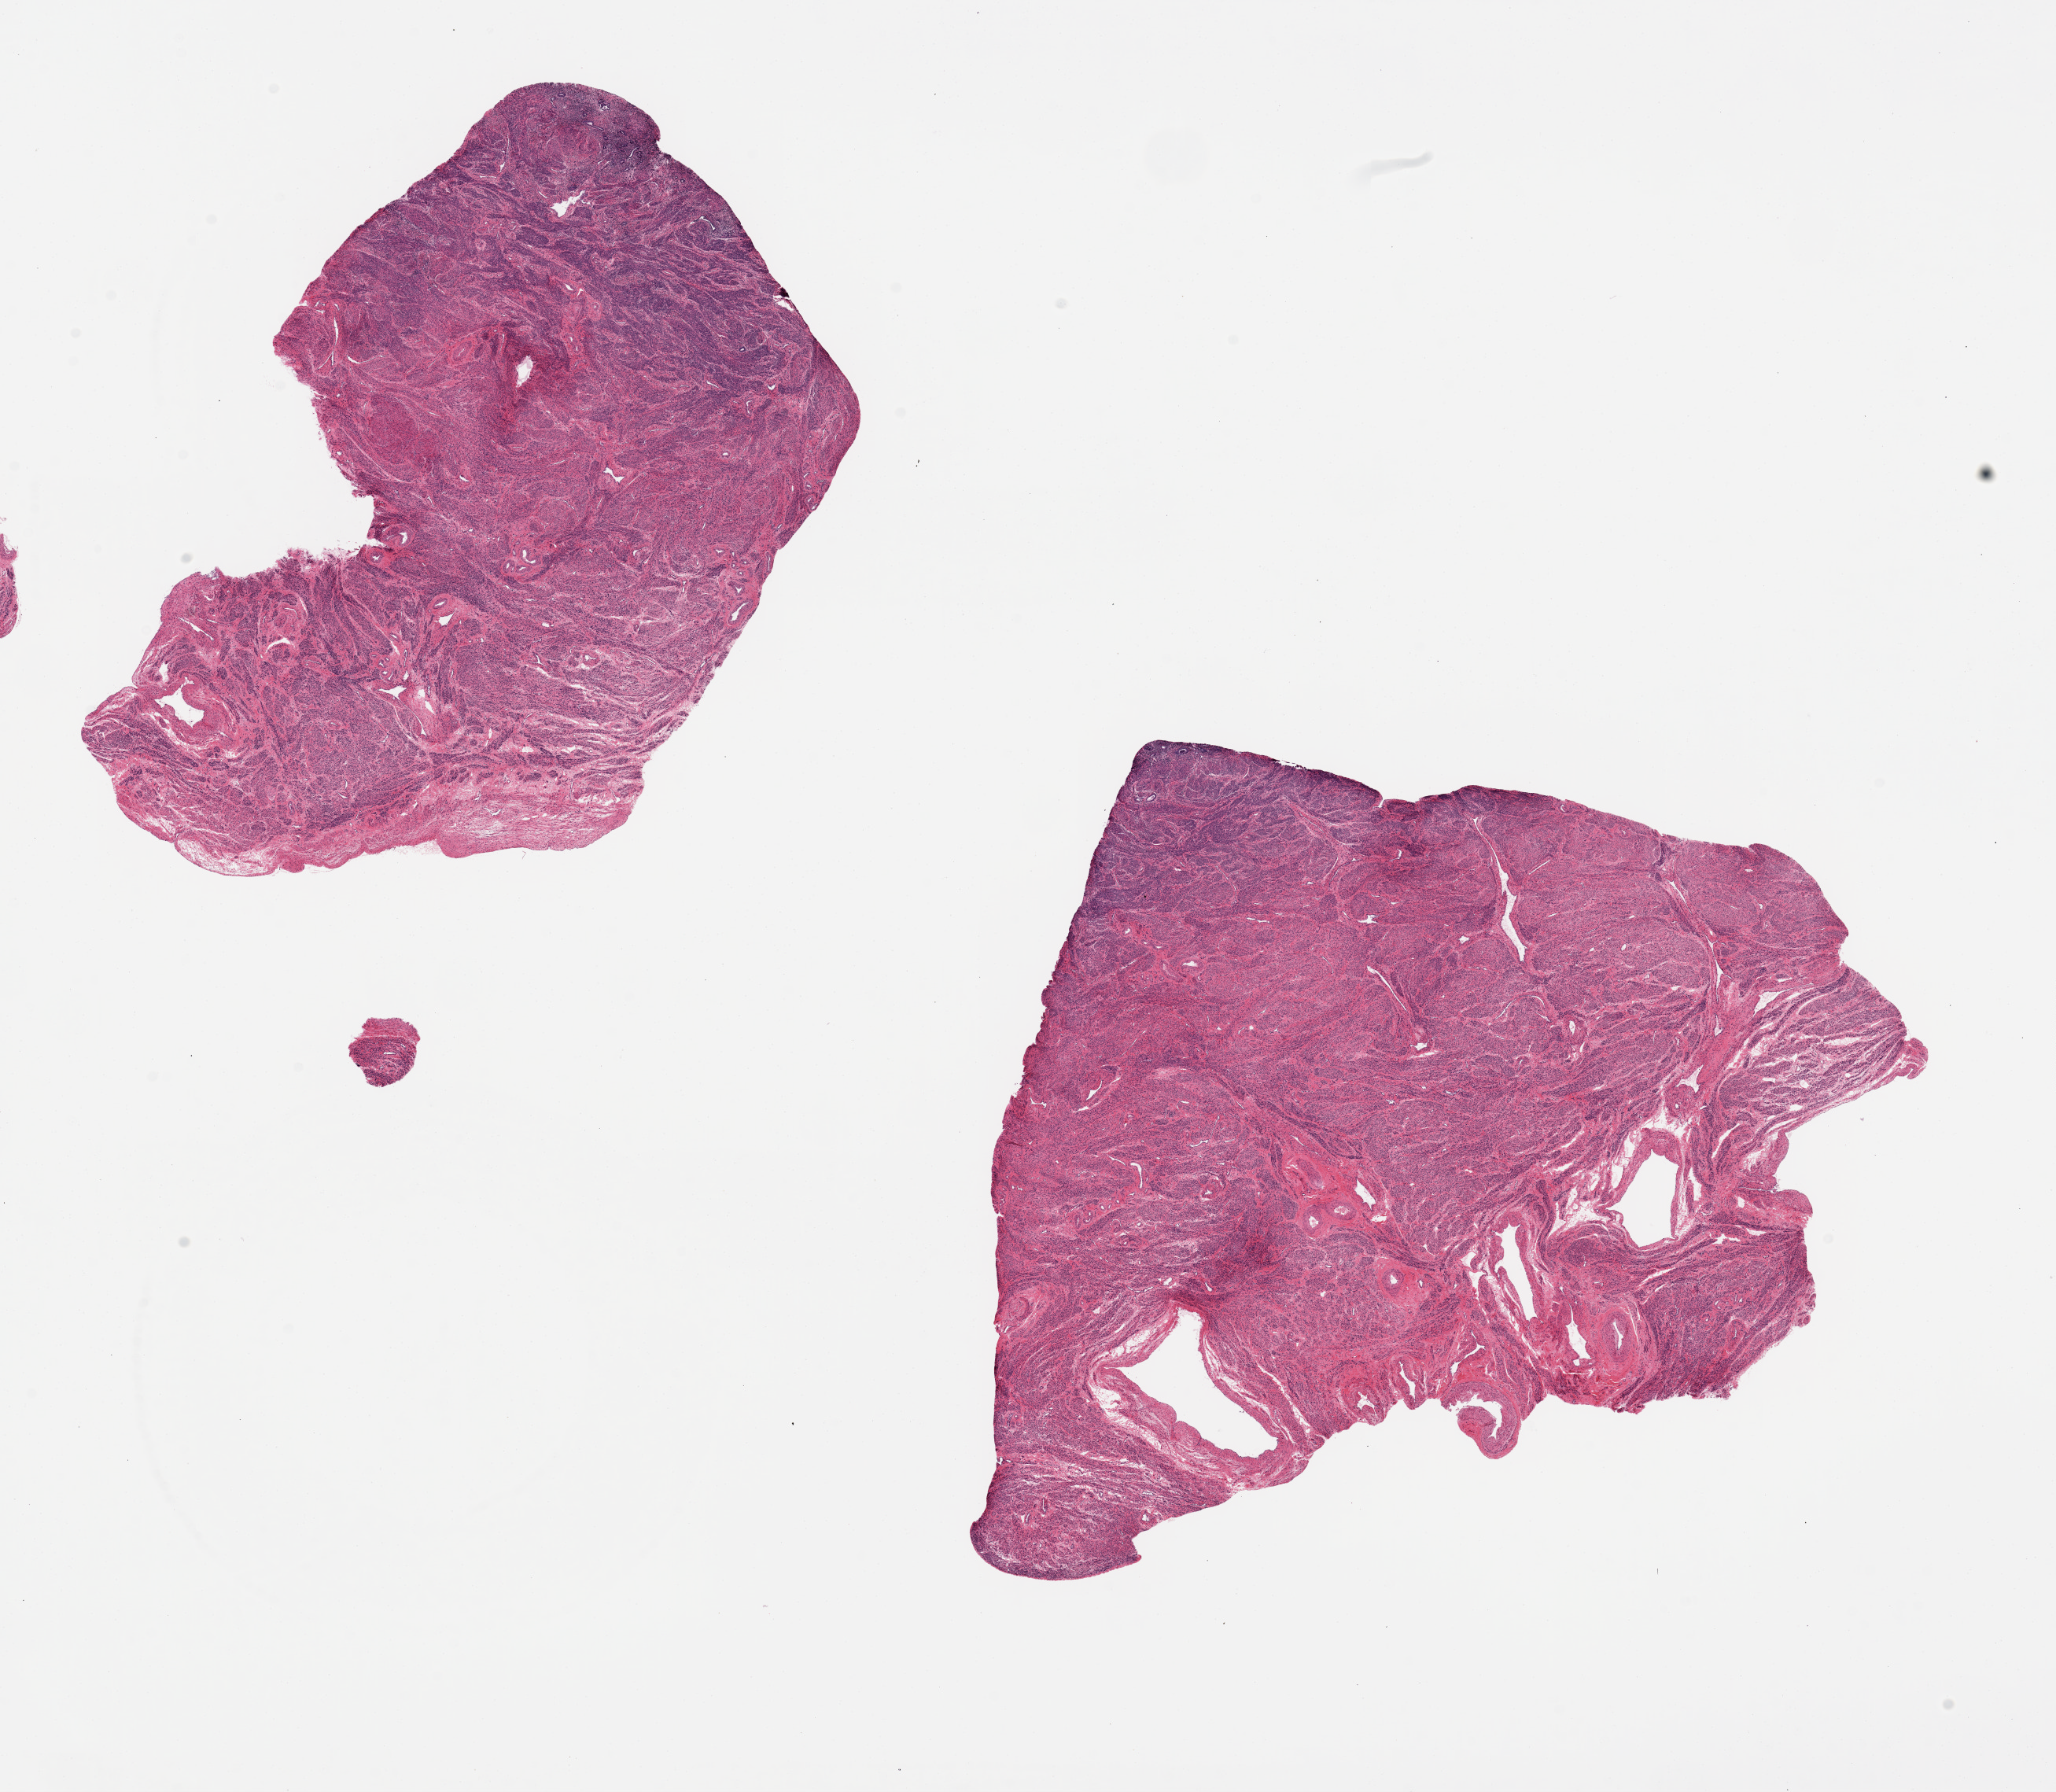
Hematoxylin and eosin (H&E) whole-slide image, shown as a low-resolution overview of the whole scanned area (about 20.7 x 18.0 mm, acquisition: 20x scan), PAXgene-fixed paraffin-embedded (PFPE) section, sampled site (target tissue): uterus, tissue donor sample.
• review note (as recorded): 2 pieces, 9x6 & 9x9mm; no endometrium, only myometrium (in these sections)